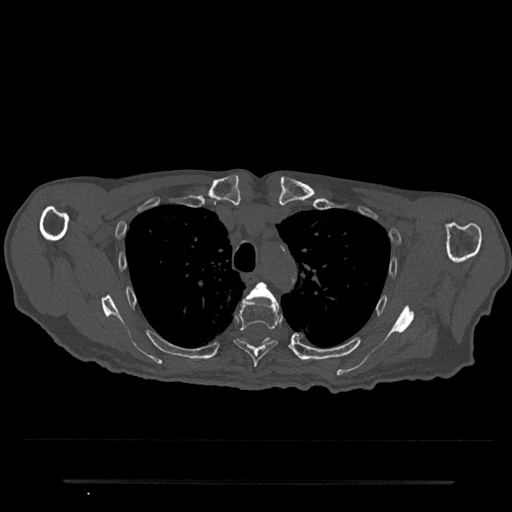
CT including the spine, one axial slice. Position 579 of 797 along the scan axis. Reconstruction kernel Br40s/3. Bone window (W 1800 / L 400 HU). 0.5 mm slice thickness. 512 × 512 image matrix, field of view 427 × 427 mm. Male patient, age 74 years. From the clinical record (not read from this slice): primary cancer: prostate.
Outlined on this slice (semi-automatically segmented with operator editing):
- T4 vertebra: bounding box [x1, y1, x2, y2] px = [247, 282, 276, 300]
- T5 vertebra: [234, 295, 282, 367]
- T6 vertebra: [242, 338, 270, 344]